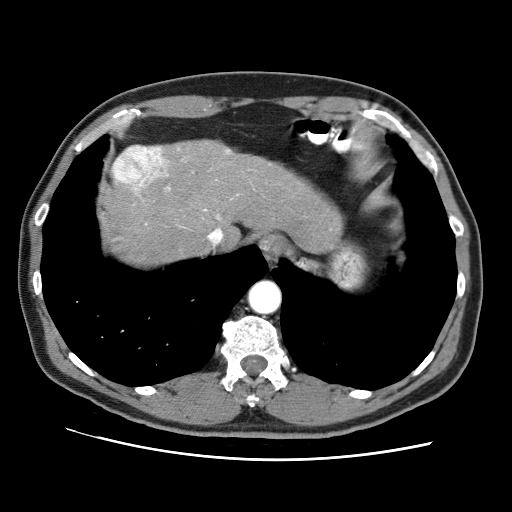
Contrast-enhanced abdominal CT (liver protocol), one axial slice; slice 60 of 71 in the series (ordered by position); soft-tissue window (W 400 / L 40 HU); 2.5 mm slice thickness; 512 × 512 image matrix, field of view 360 × 360 mm. Case-level facts recorded for this patient, not image findings: diagnosis: hepatocellular carcinoma (patient treated with transarterial chemoembolisation; whether this scan precedes or follows treatment is not stated here); TNM stage (as recorded): Stage-II; Child-Pugh class: A; tumour differentiation: well differentiated; tumour size: 4.6 cm.
Structures marked on this image (semi-automatically segmented with operator editing):
- liver parenchyma outside the tumour (the mass and vessels are separate outlines, so this box may not span the whole liver): bounding box <102,140,334,264> (left, top, right, bottom; pixels)
- mass: <114,144,174,192>
- liver vessels: <124,149,230,190>